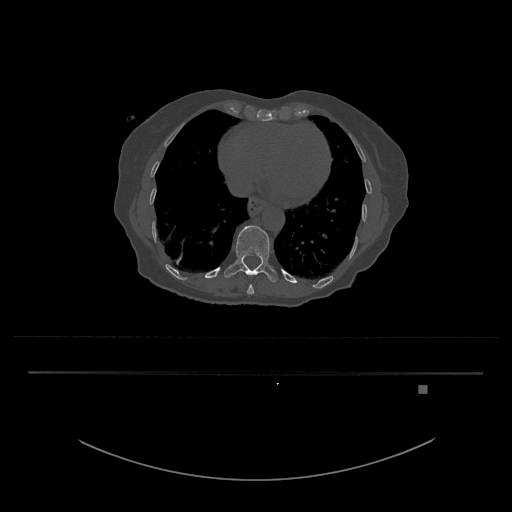
CT including the spine, one axial slice. Slice 675 of 797 in the series (ordered by position). Reconstruction kernel Br40s/3. 120 kVp. Bone window (W 1800 / L 400 HU). 0.5 mm slice thickness. 512 × 512 image matrix. Patient: female, 57 years. From the clinical record (not read from this slice): primary cancer: cervical.
Outlined on this slice (semi-automatic segmentation, software-assisted and operator-edited):
- T10 vertebra: bounding box [x1, y1, x2, y2] px = [247, 274, 255, 294]
- T11 vertebra: [224, 225, 278, 282]